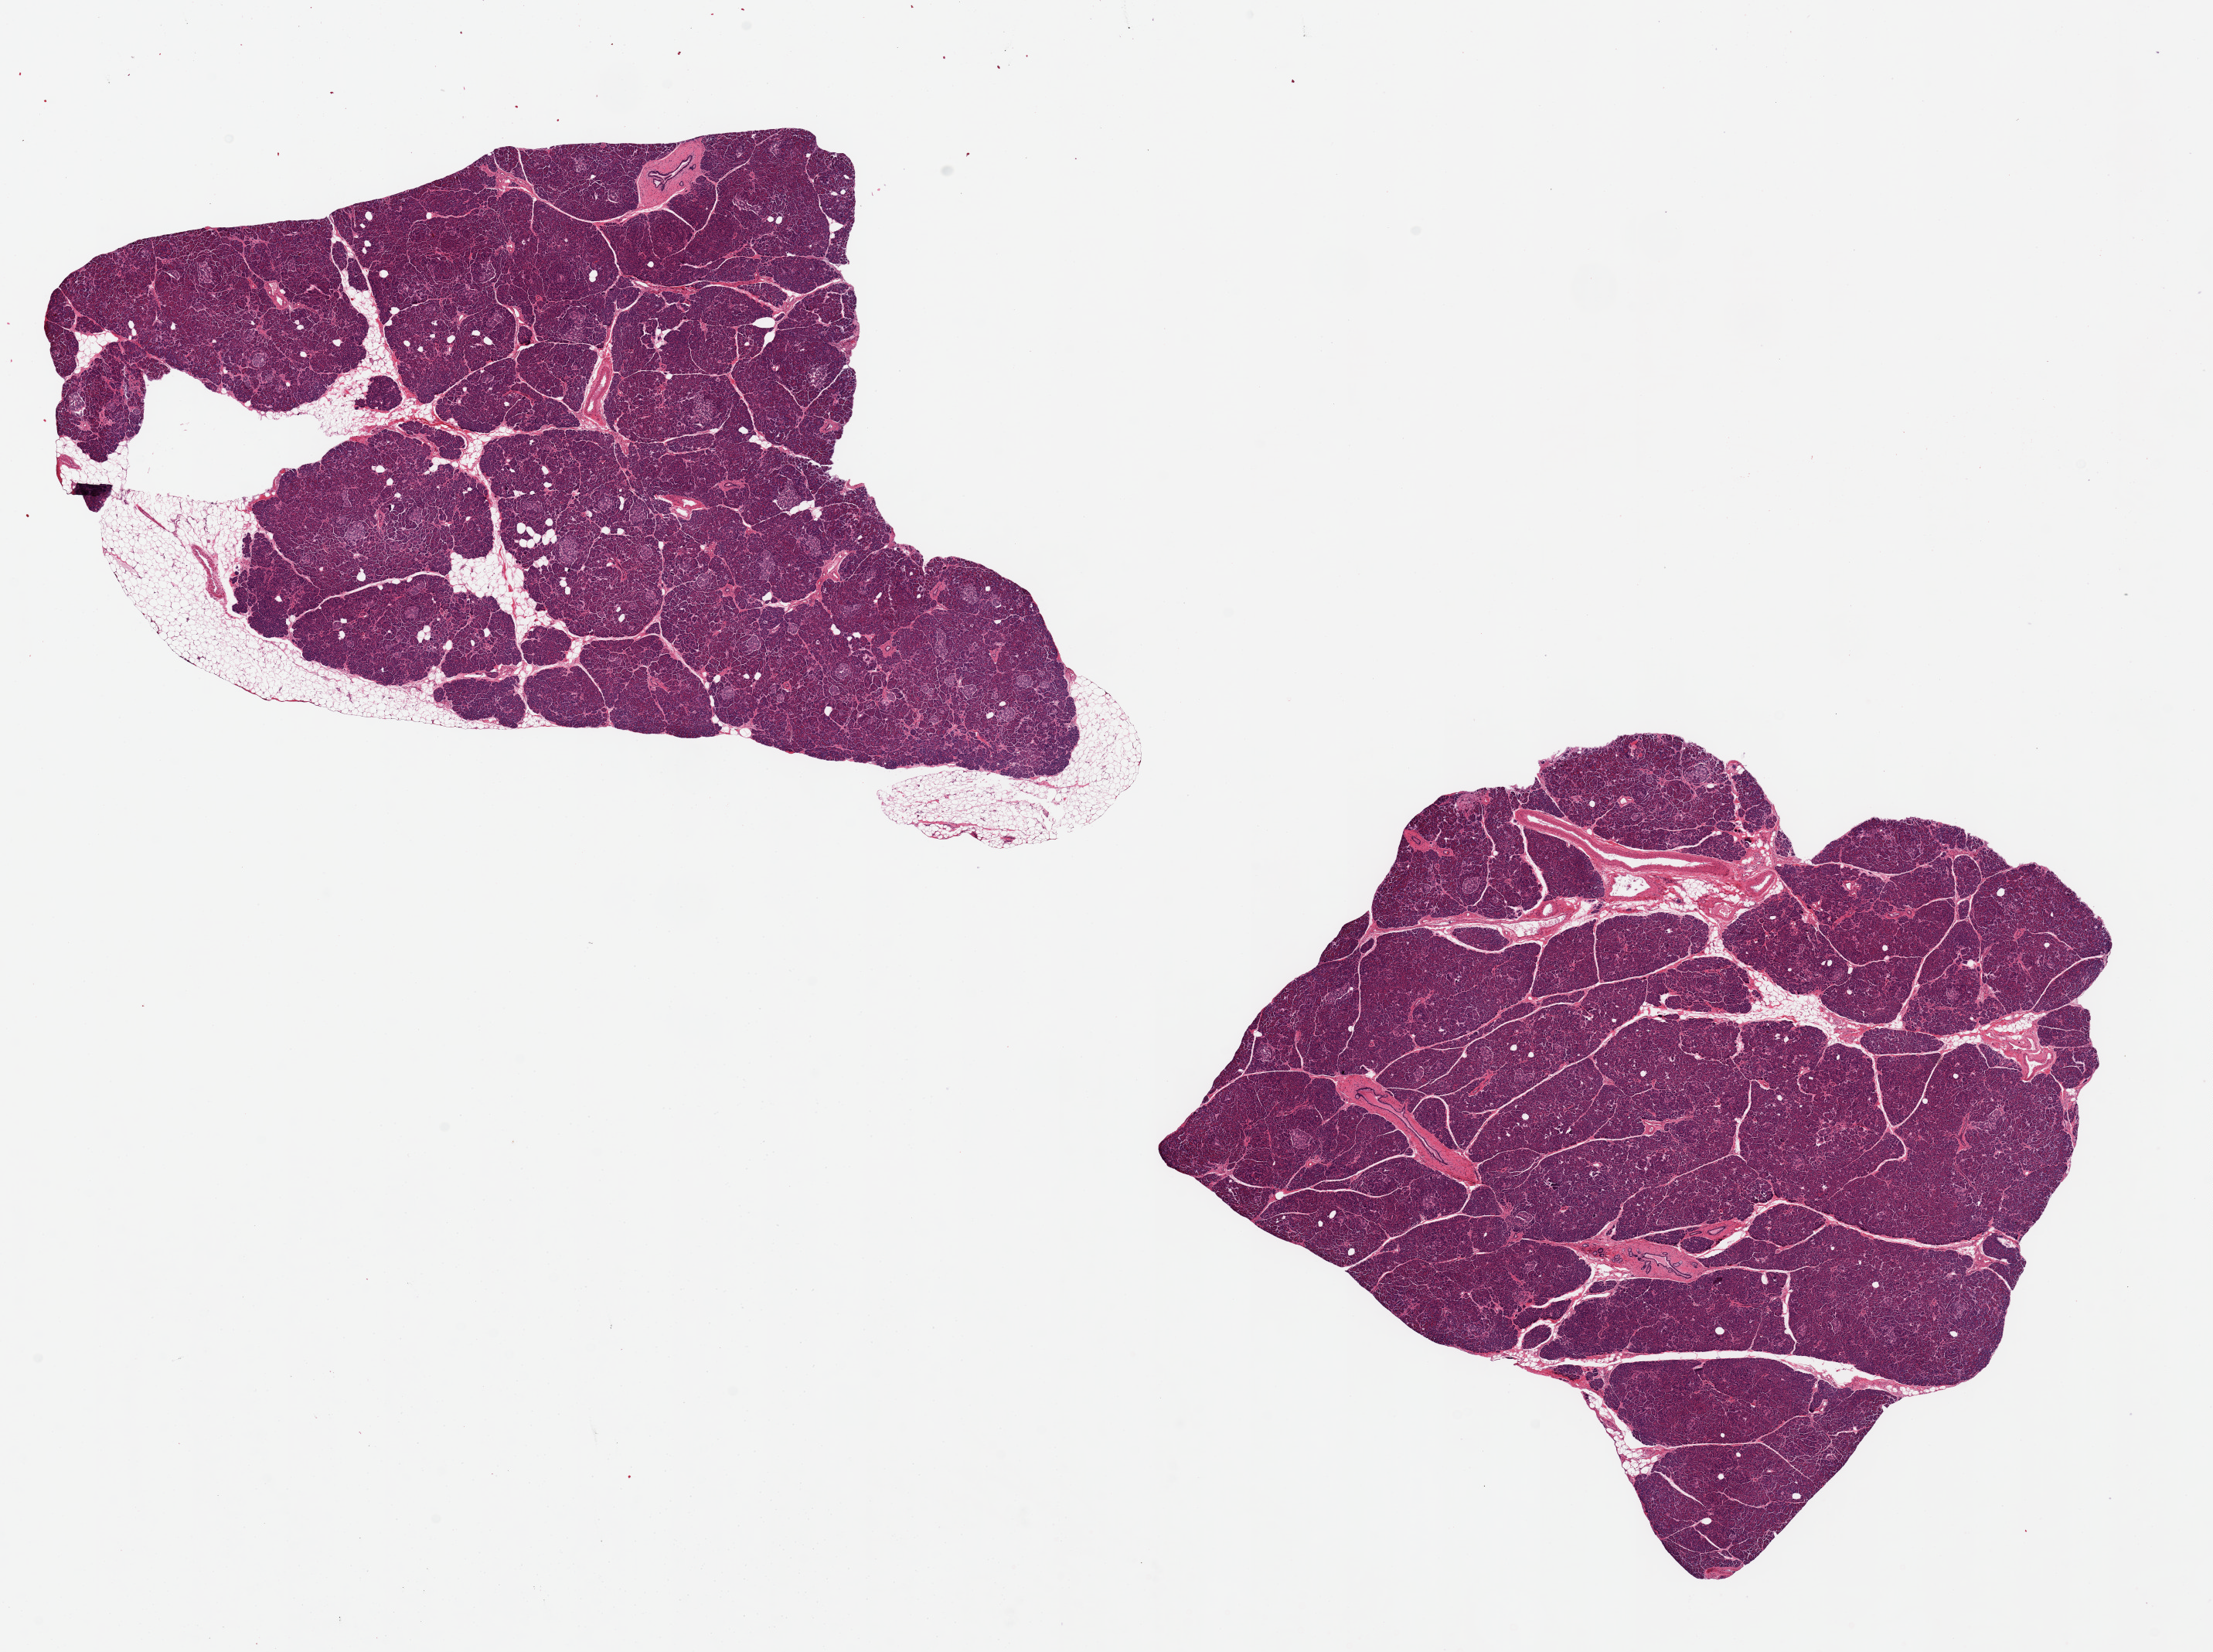
Haematoxylin and eosin whole-slide image, brightfield, a low-resolution overview of the entire scanned area, about 22.6 x 16.9 mm; PAXgene-fixed, paraffin-embedded tissue; target tissue: pancreas; tissue donor sample. Donor sex: male.
Review note (as recorded): 2 pieces, 11x7 & 8x8mm; 10% adipose in one, none in the other; many islets.